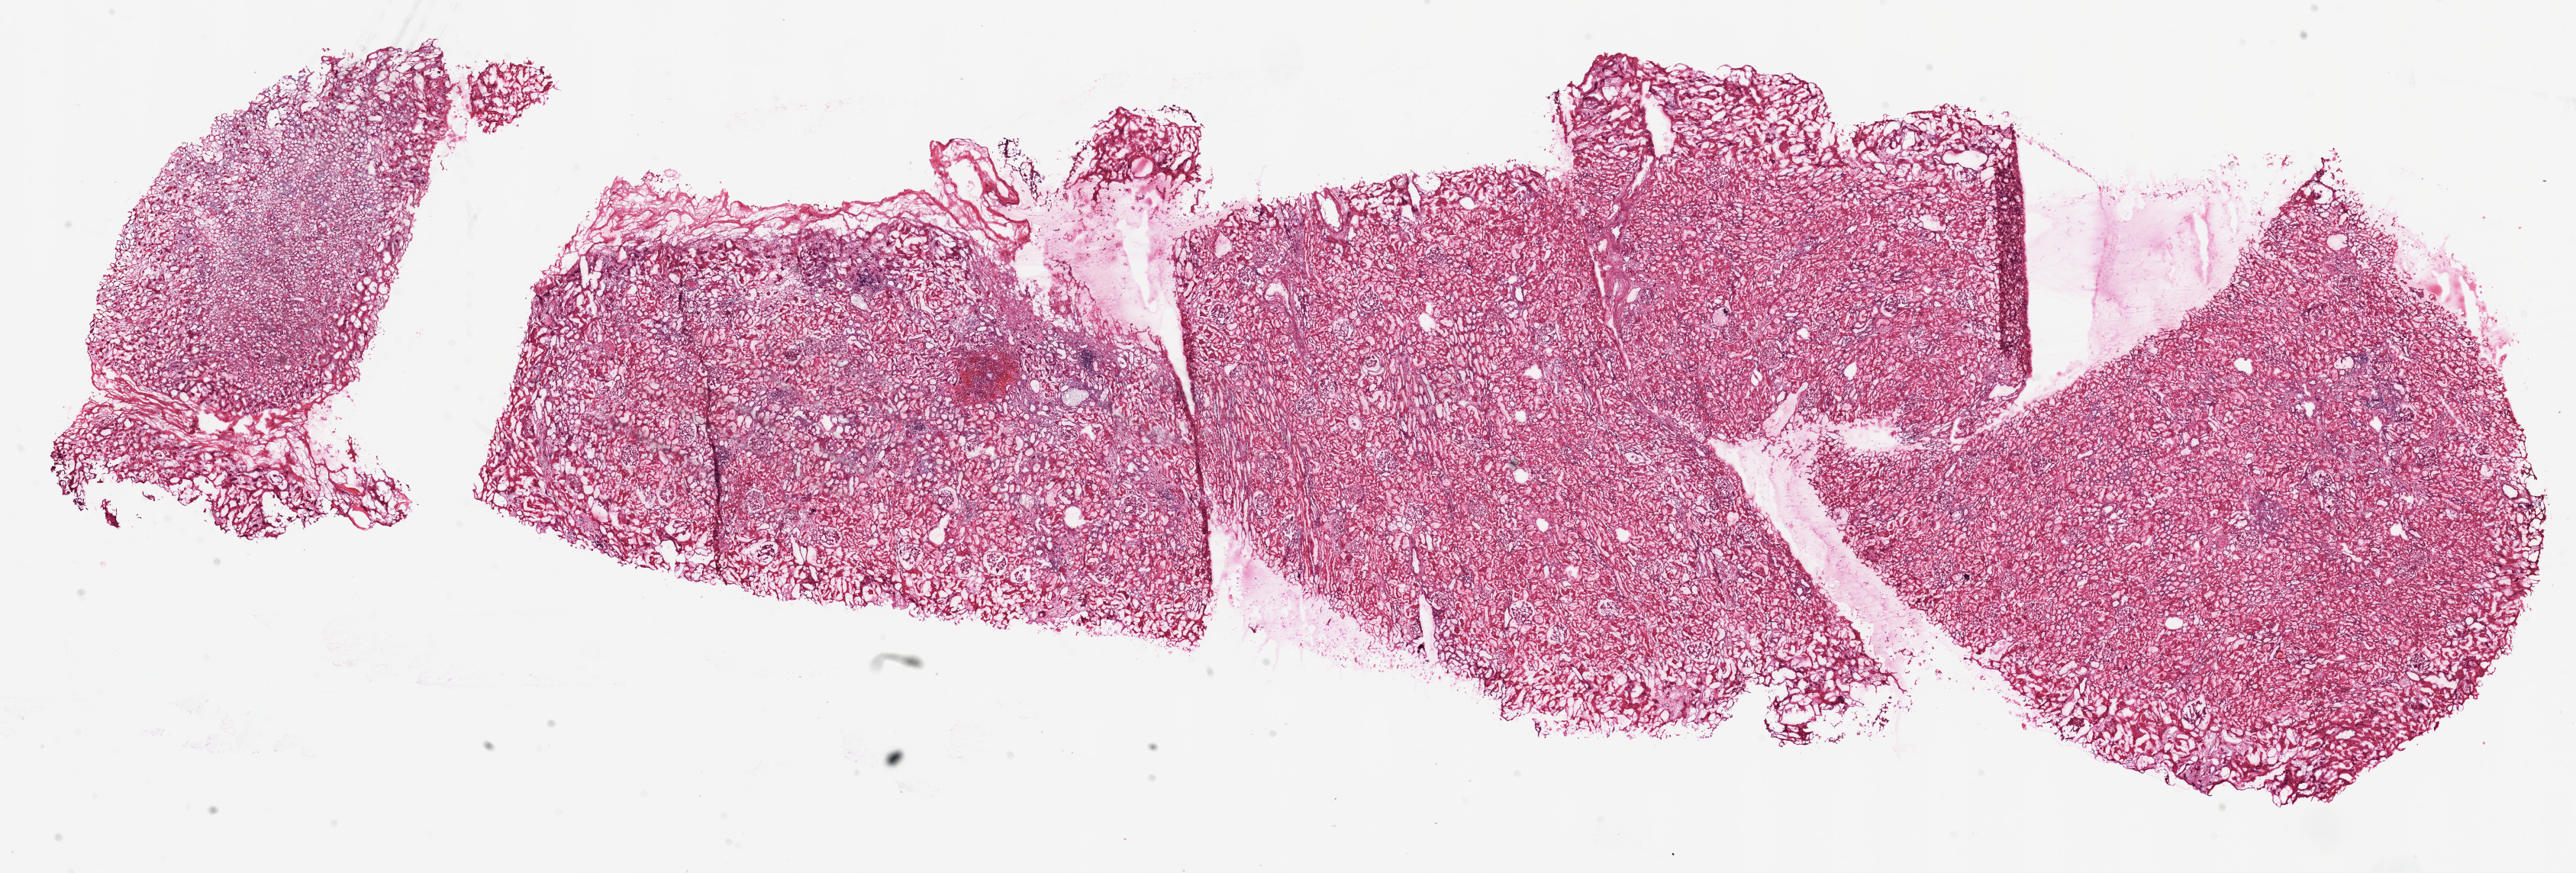
Whole-slide histology image, H&E-stained, whole scanned area (about 27.1 x 9.2 mm, slide scanned at 20x) shown as a low-resolution overview; frozen section from the top of the tissue portion; sample: solid tissue normal (non-tumour tissue), kidney. Patient: male, age at initial diagnosis 58 years.
This section: solid tissue normal sample (biorepository sample class). Patient diagnosis: Clear cell adenocarcinoma, NOS.